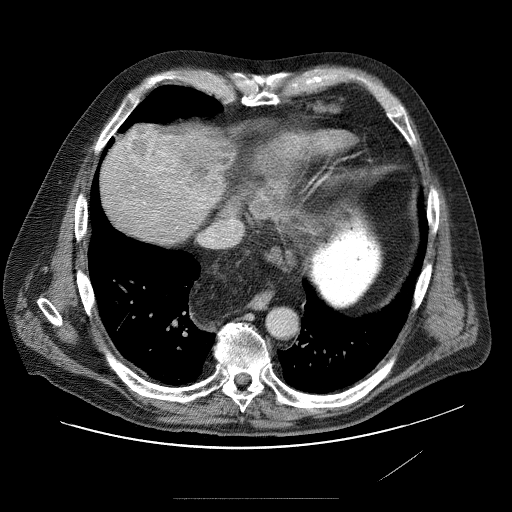
Contrast-enhanced abdominal CT (liver protocol), one axial slice; position 75 of 89 along the scan axis; 120 kVp; soft-tissue window (W 400 / L 40 HU); 2.5 mm slice thickness; 512 × 512 image matrix, field of view 420 × 420 mm. Case-level facts recorded for this patient, not image findings: diagnosis: hepatocellular carcinoma (patient treated with transarterial chemoembolisation; whether this scan precedes or follows treatment is not stated here); TNM stage (as recorded): Stage-IVA; Child-Pugh class: A; tumour differentiation: moderately differentiated.
Structures marked on this image (semi-automatic segmentation, software-assisted and operator-edited):
- liver parenchyma outside the tumour (the mass and vessels are separate outlines, so this box may not span the whole liver): bounding box [x1, y1, x2, y2] px = [104, 128, 218, 230]
- mass: [131, 129, 225, 218]
- liver vessels: [118, 157, 149, 211]